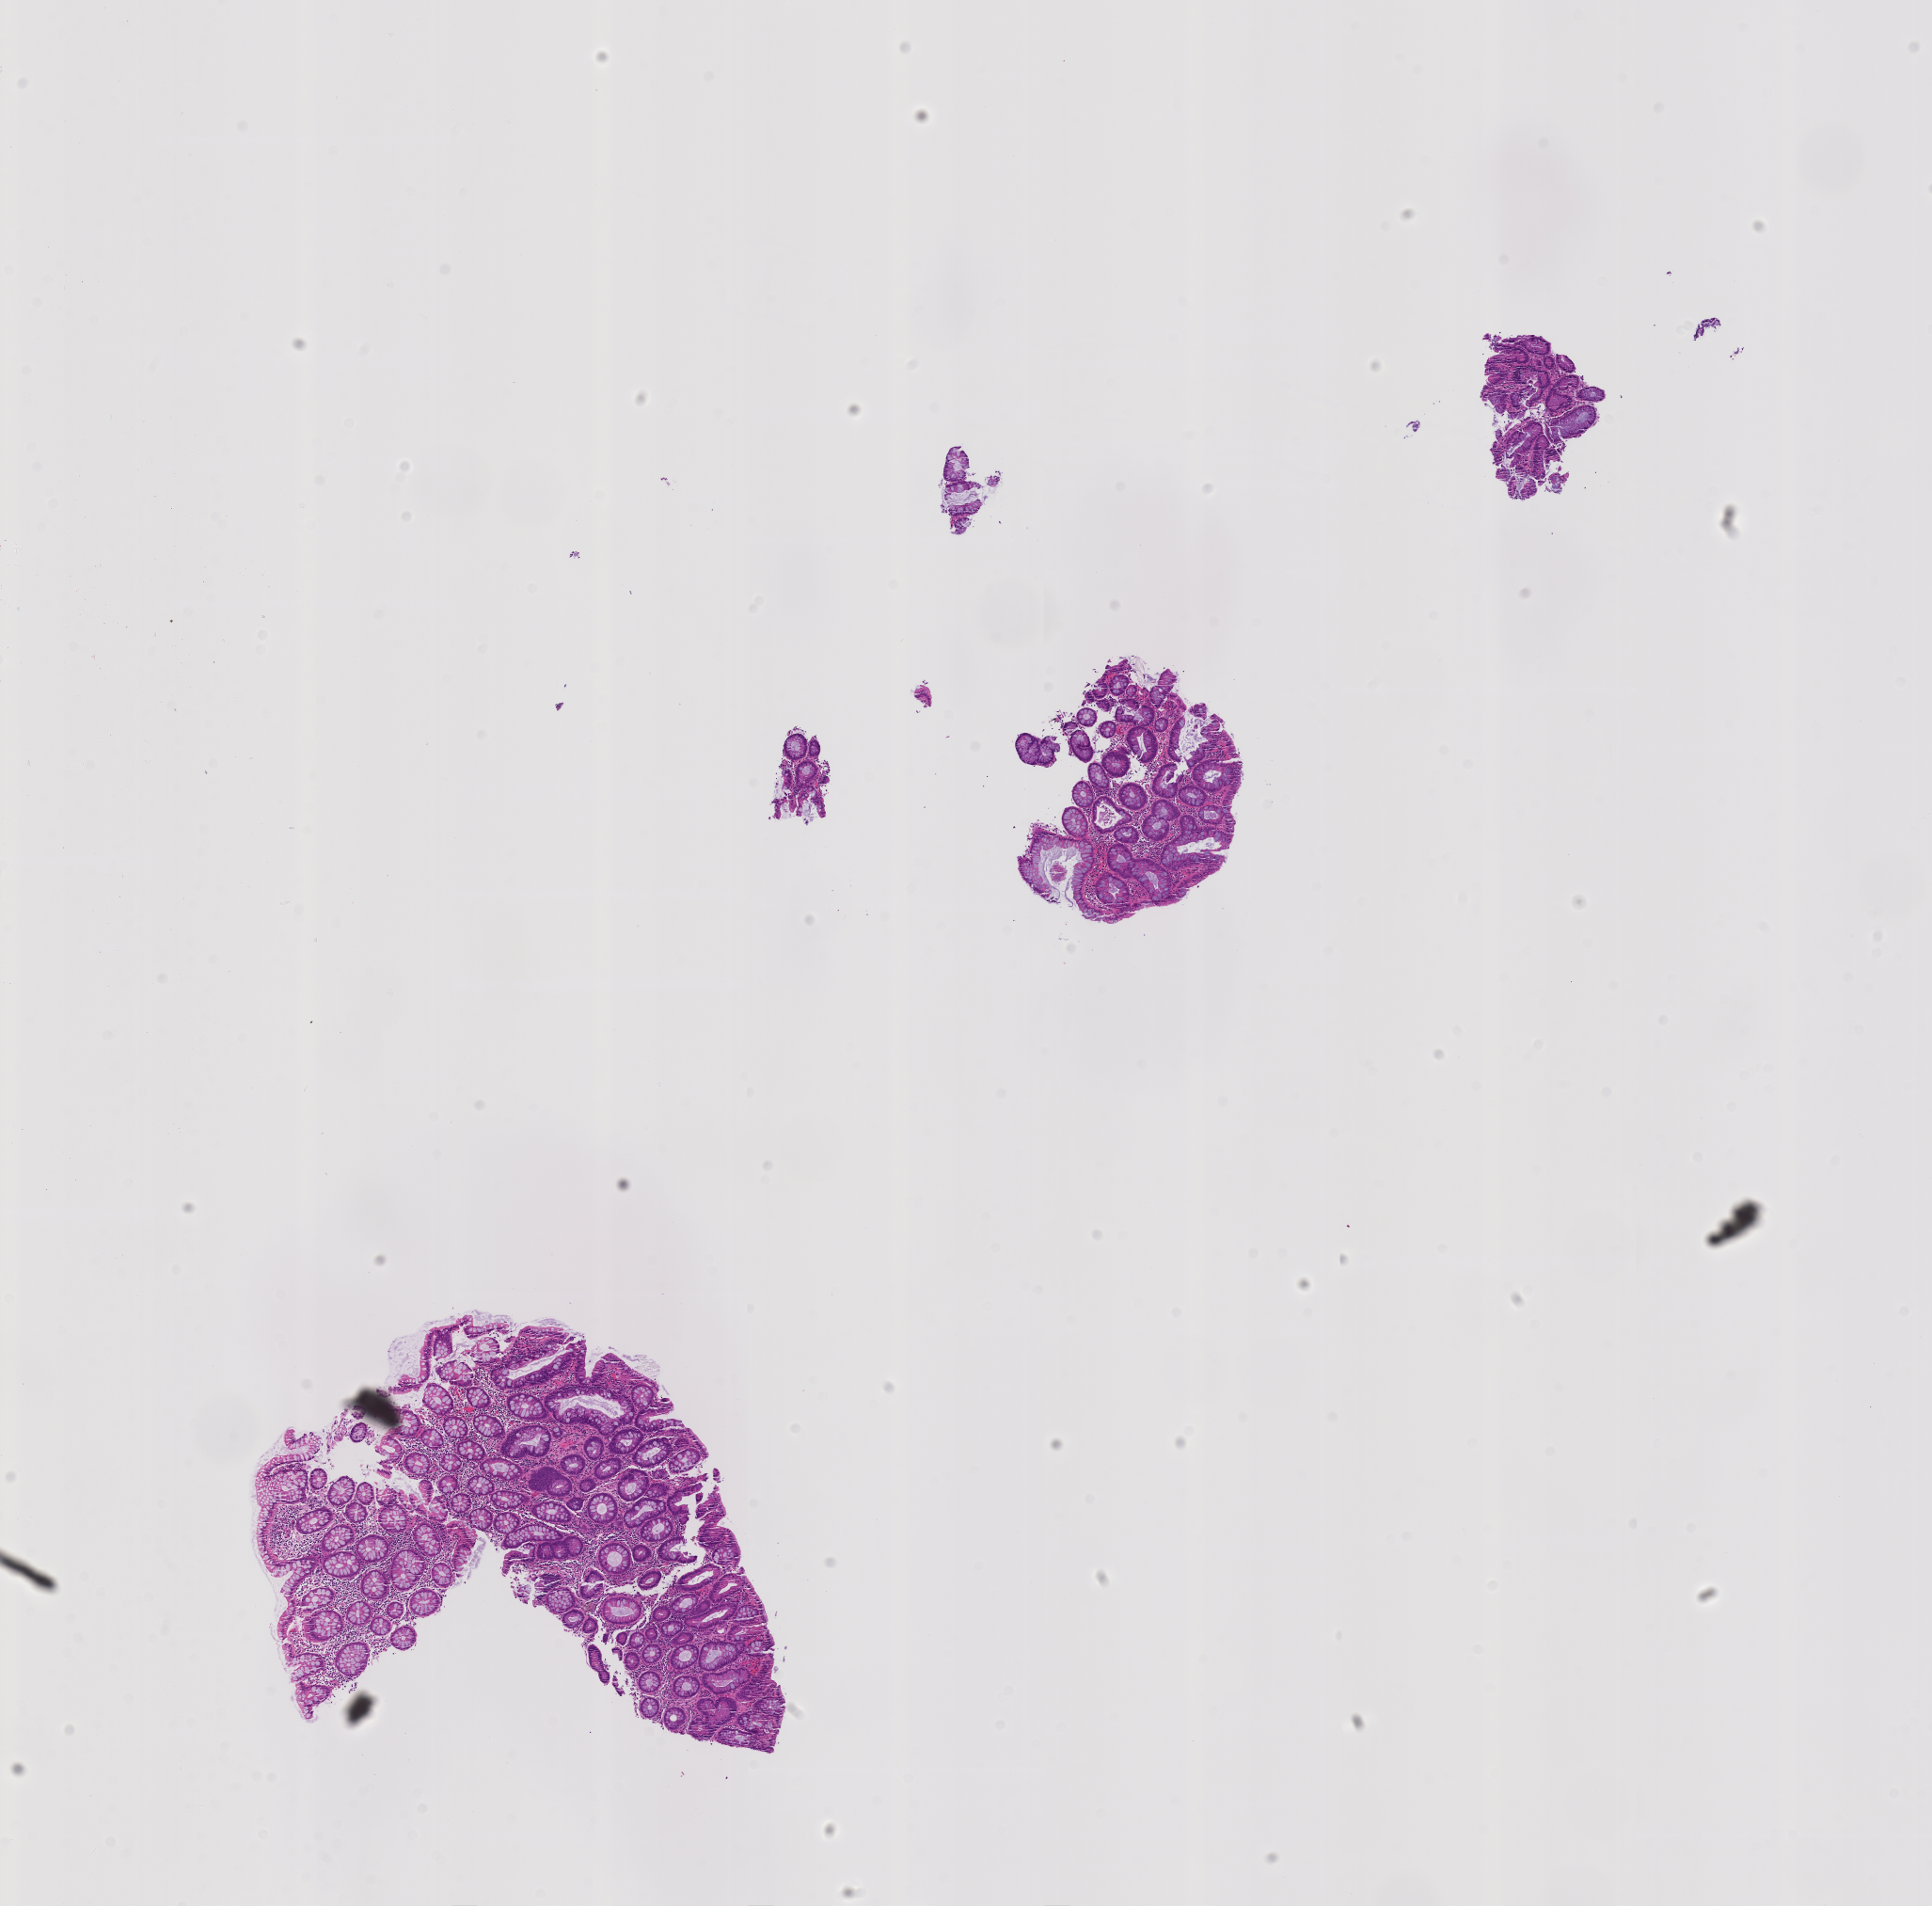
Whole-slide image, H&E stain: colon biopsy, low-resolution overview of the scanned area, about 8.2 x 8.1 mm. Formalin-fixed, paraffin-embedded (FFPE) tissue. Site: hepatic flexure of colon. Patient sex: female.
Lesion category (as recorded): premalignant.